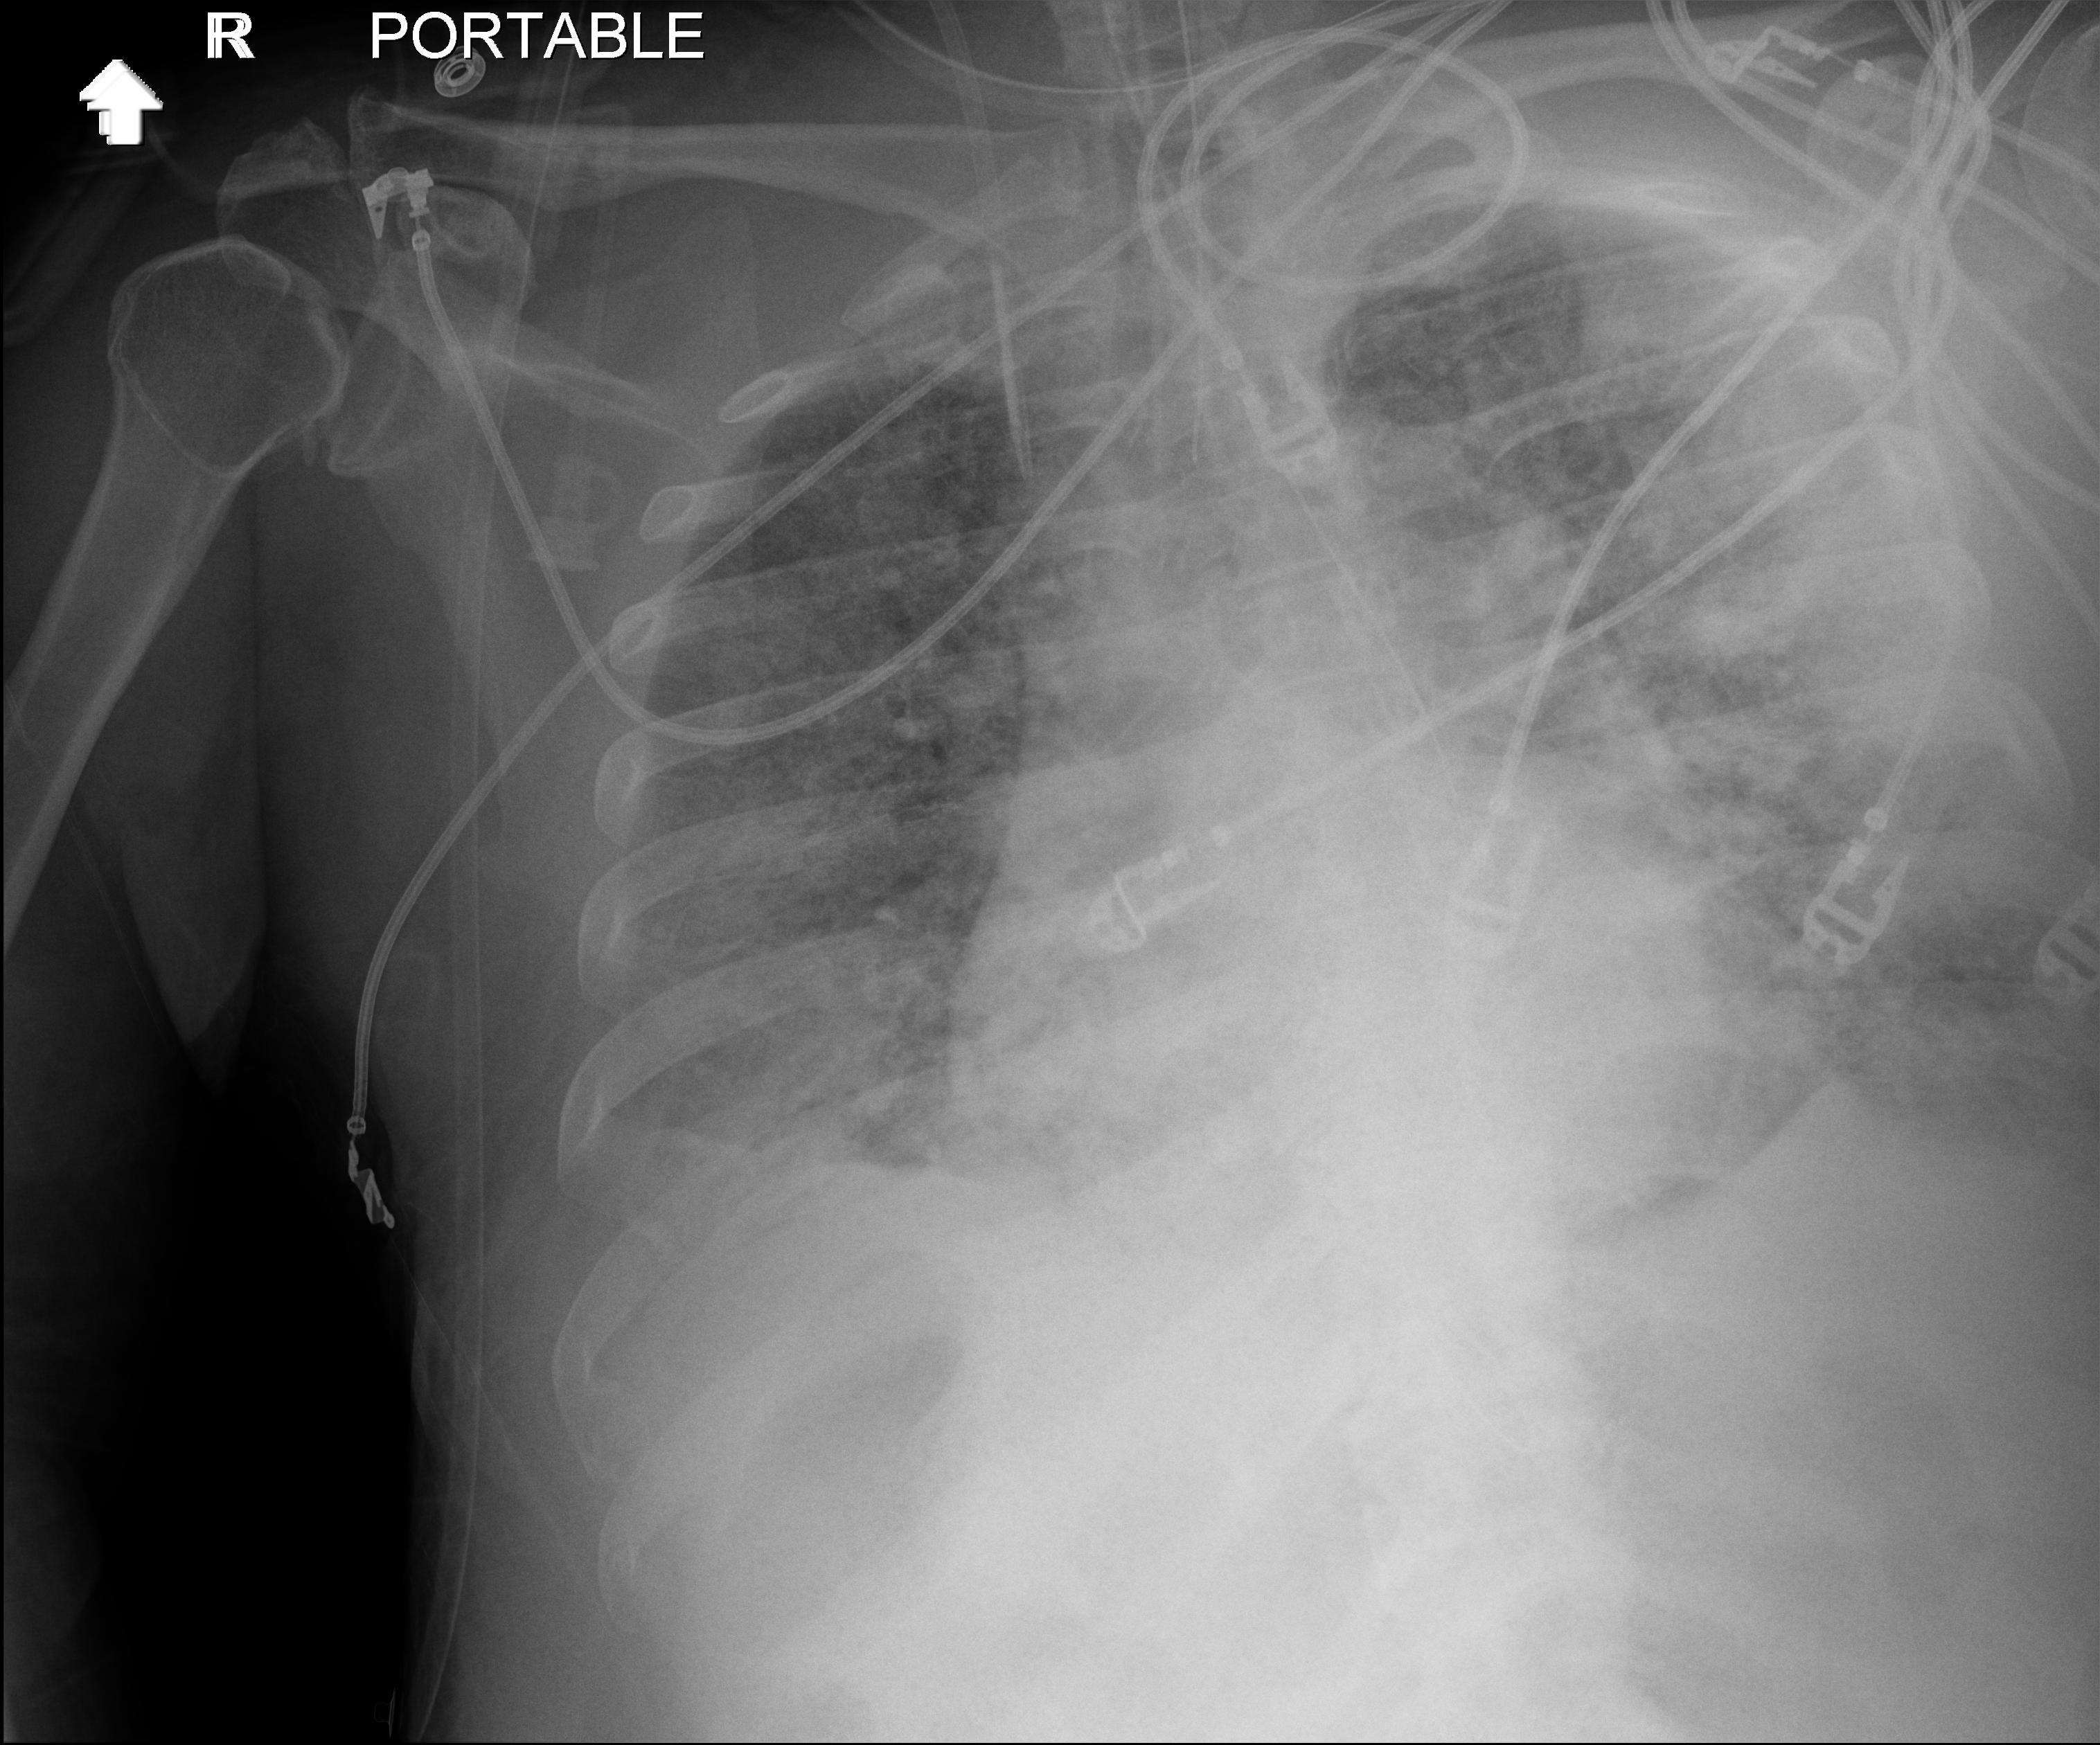
Bedside chest radiograph (digital radiography); anteroposterior (AP) projection. Patient hospitalised with COVID-19; male, aged 60–74 years.
From the hospital-stay record, not from the radiograph (when in the stay this image was taken is not recorded):
- length of hospital stay: 28 days
- admitted to intensive care during this hospital stay: yes
- mechanically ventilated during this hospital stay: yes